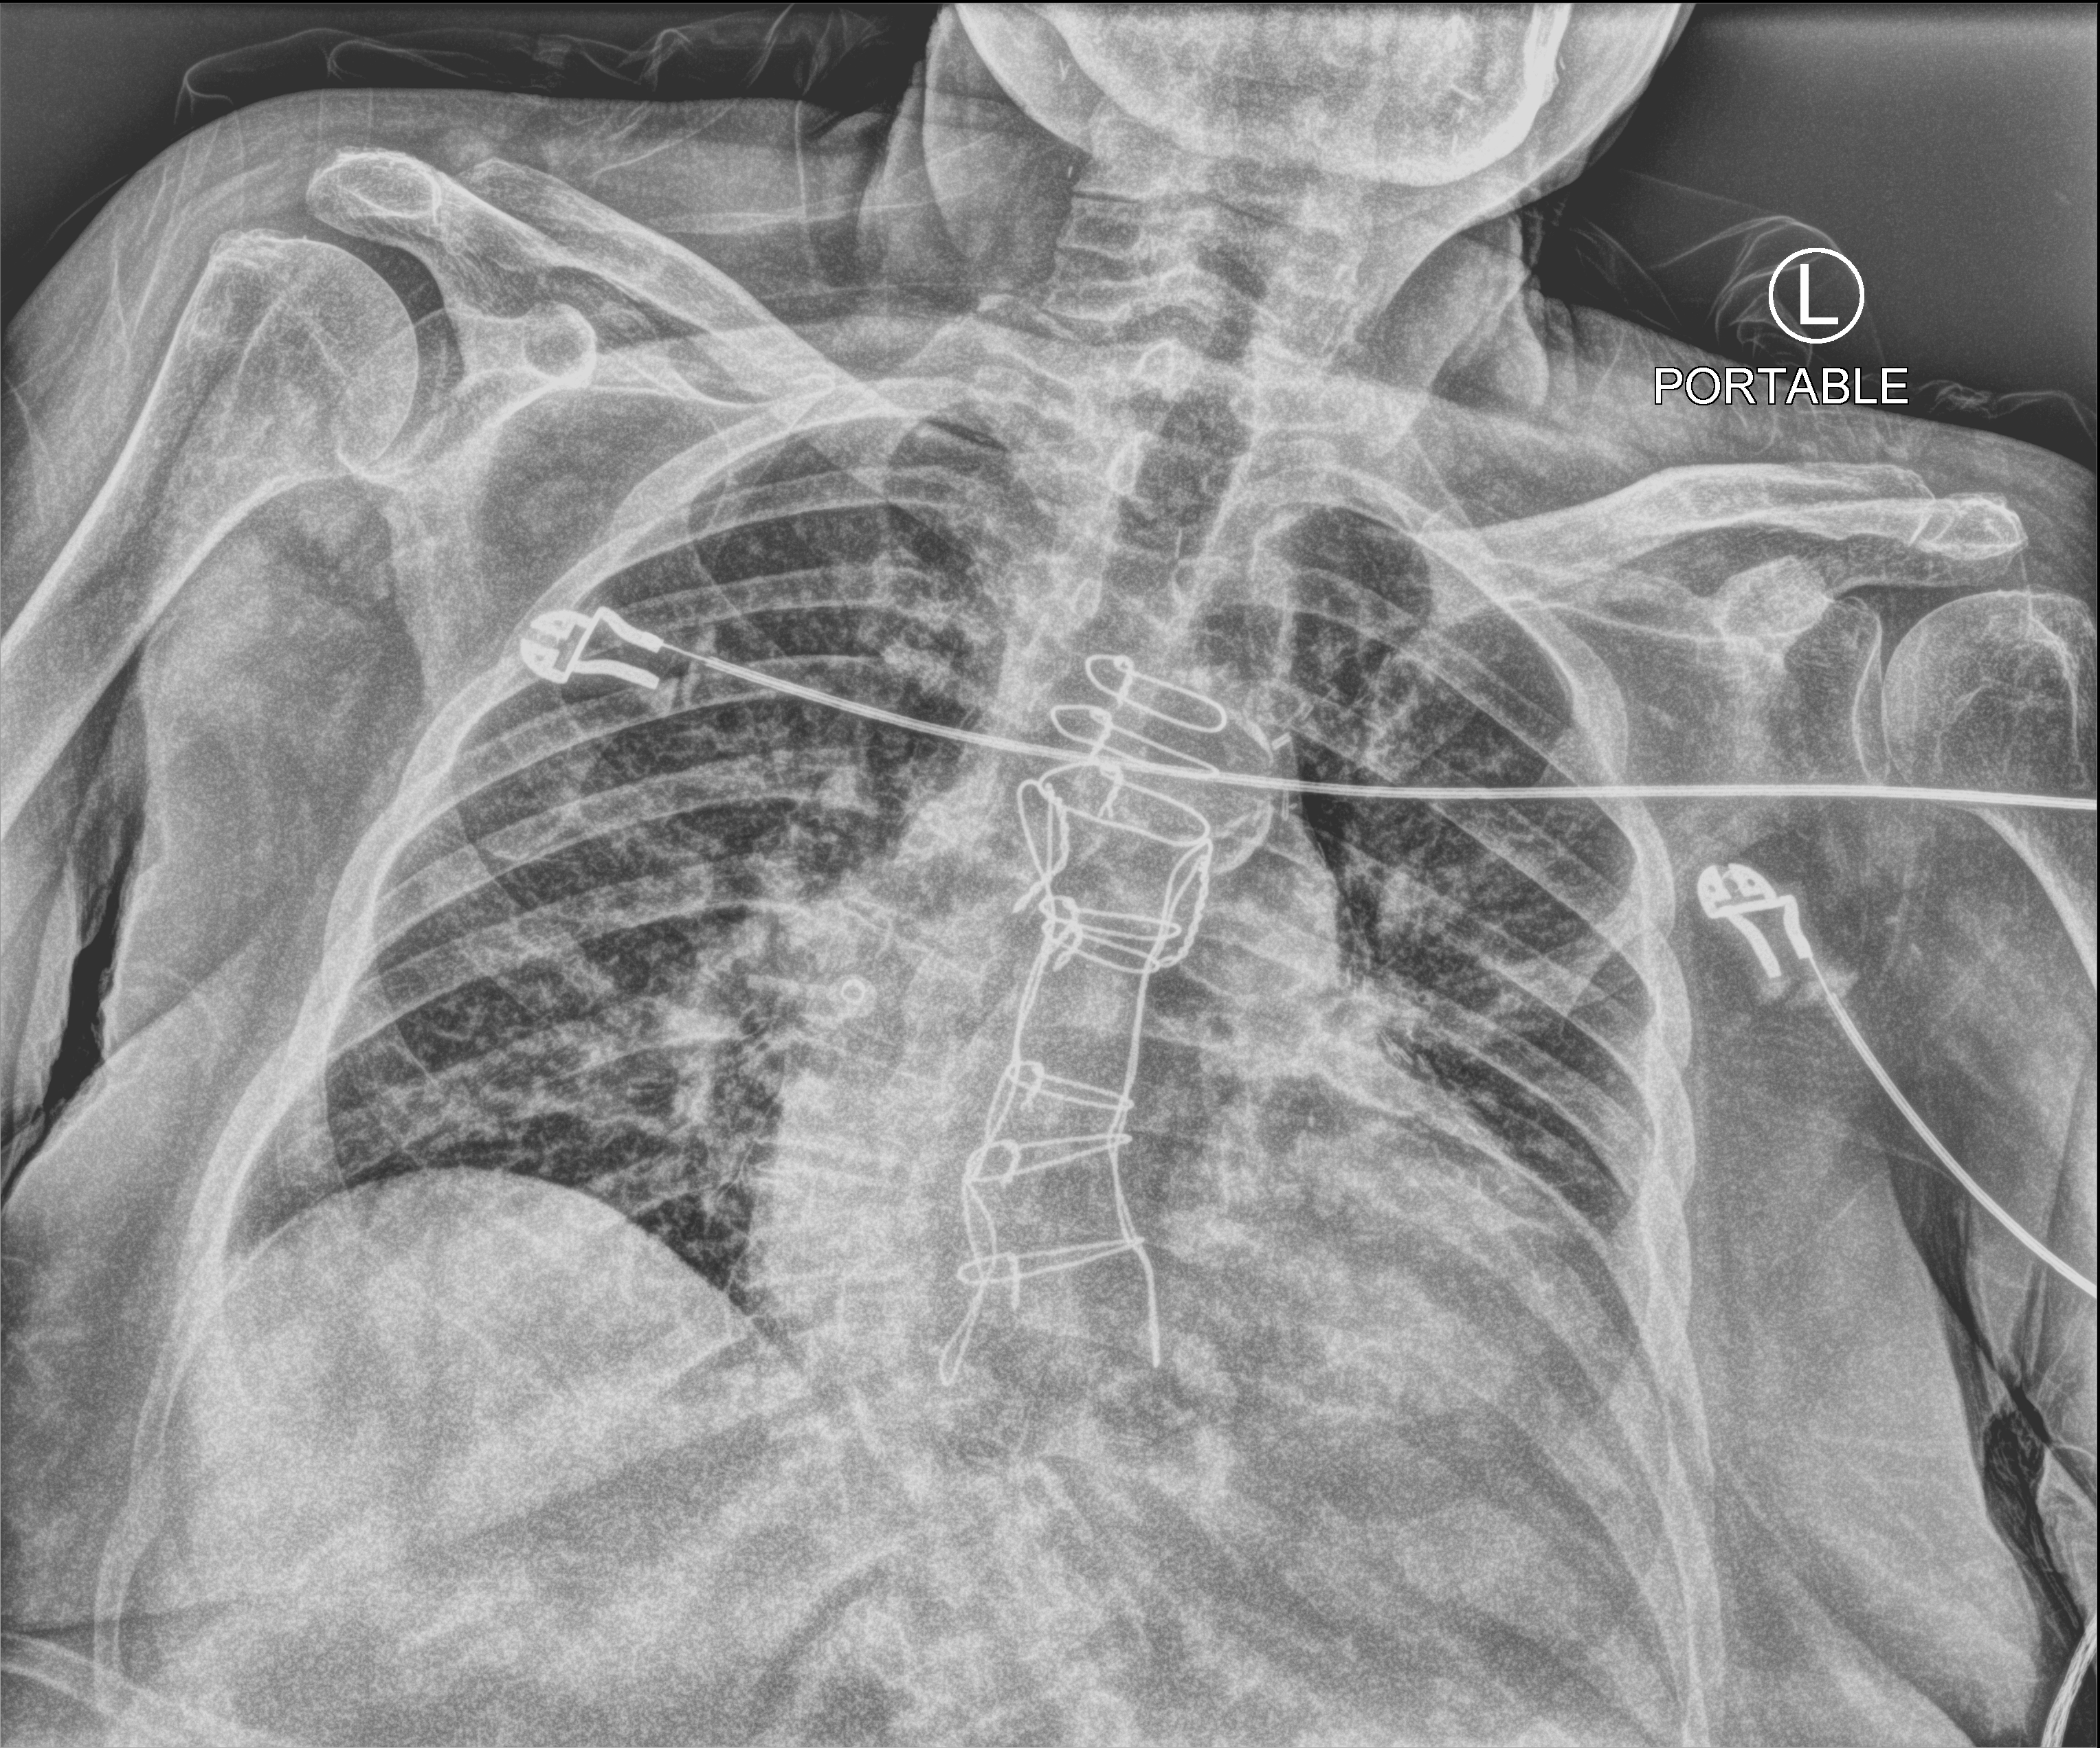
Chest X-ray (portable); anteroposterior (AP) projection. Female patient hospitalised with COVID-19, age 75–90 years.
Hospital-stay facts (about this admission, not read from this image; timing relative to this image not recorded):
- admitted to intensive care during this hospital stay: no